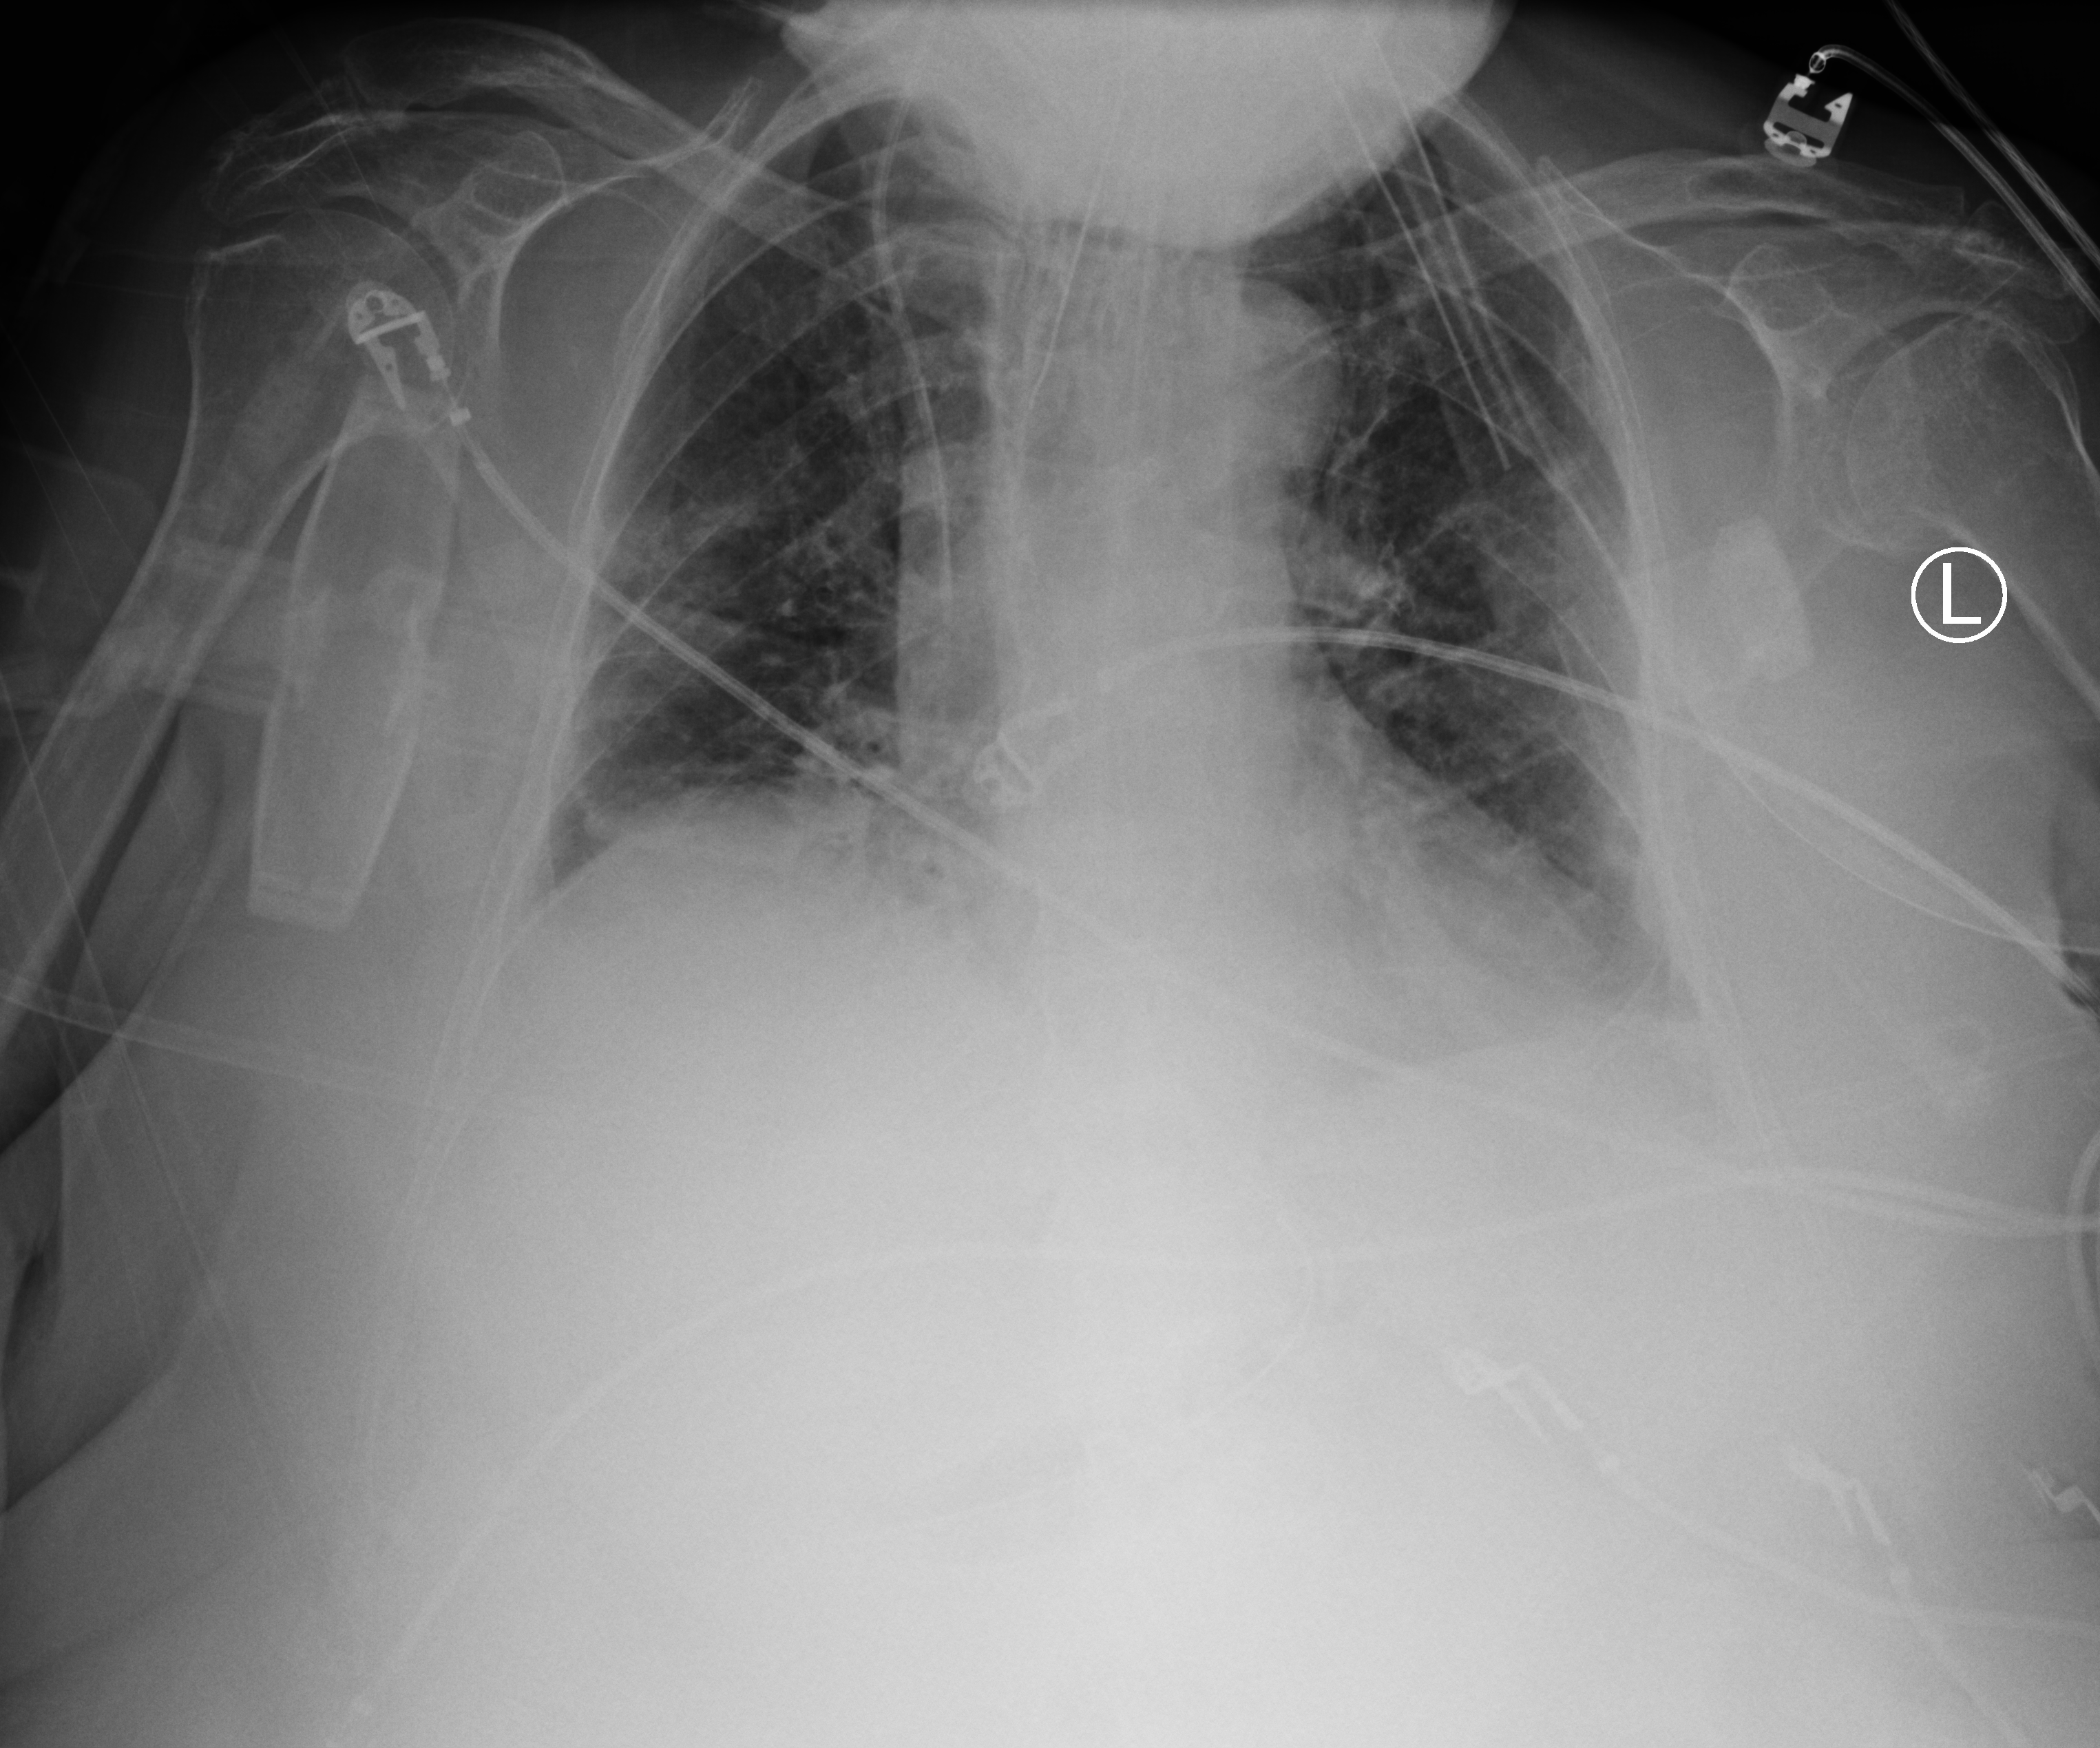
Bedside chest radiograph (computed radiography); anteroposterior (AP) projection. Patient hospitalised with COVID-19; female, aged 75–90 years.
Admission-level facts for this patient (not findings on this image; timing relative to this image not recorded): diabetes (admission record): no.